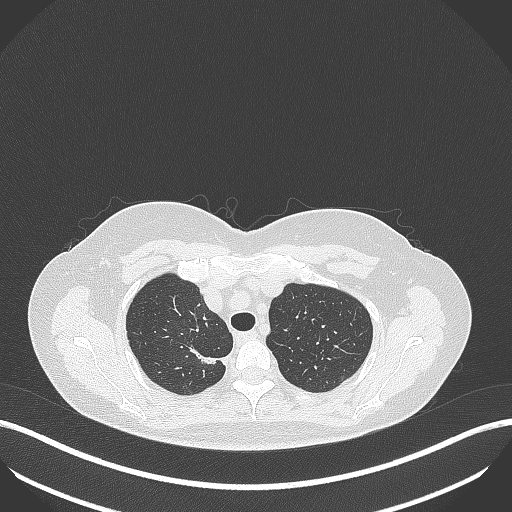
Chest CT, one axial slice. Position 321 of 386 along the scan axis. Reconstruction kernel B70f. Lung window (W 1500 / L -600 HU). 1 mm slice thickness. 512 × 512 image matrix, field of view 400 × 400 mm. Patient: female, 65 years. From the clinical record (not read from this slice): clinical TNM (as recorded): T1b N0 M0.
Structures marked on this image (rectangle marked by the reading radiologist):
- lung tumour (recorded histology: adenocarcinoma): box from (x=184, y=340) to (x=221, y=369) px